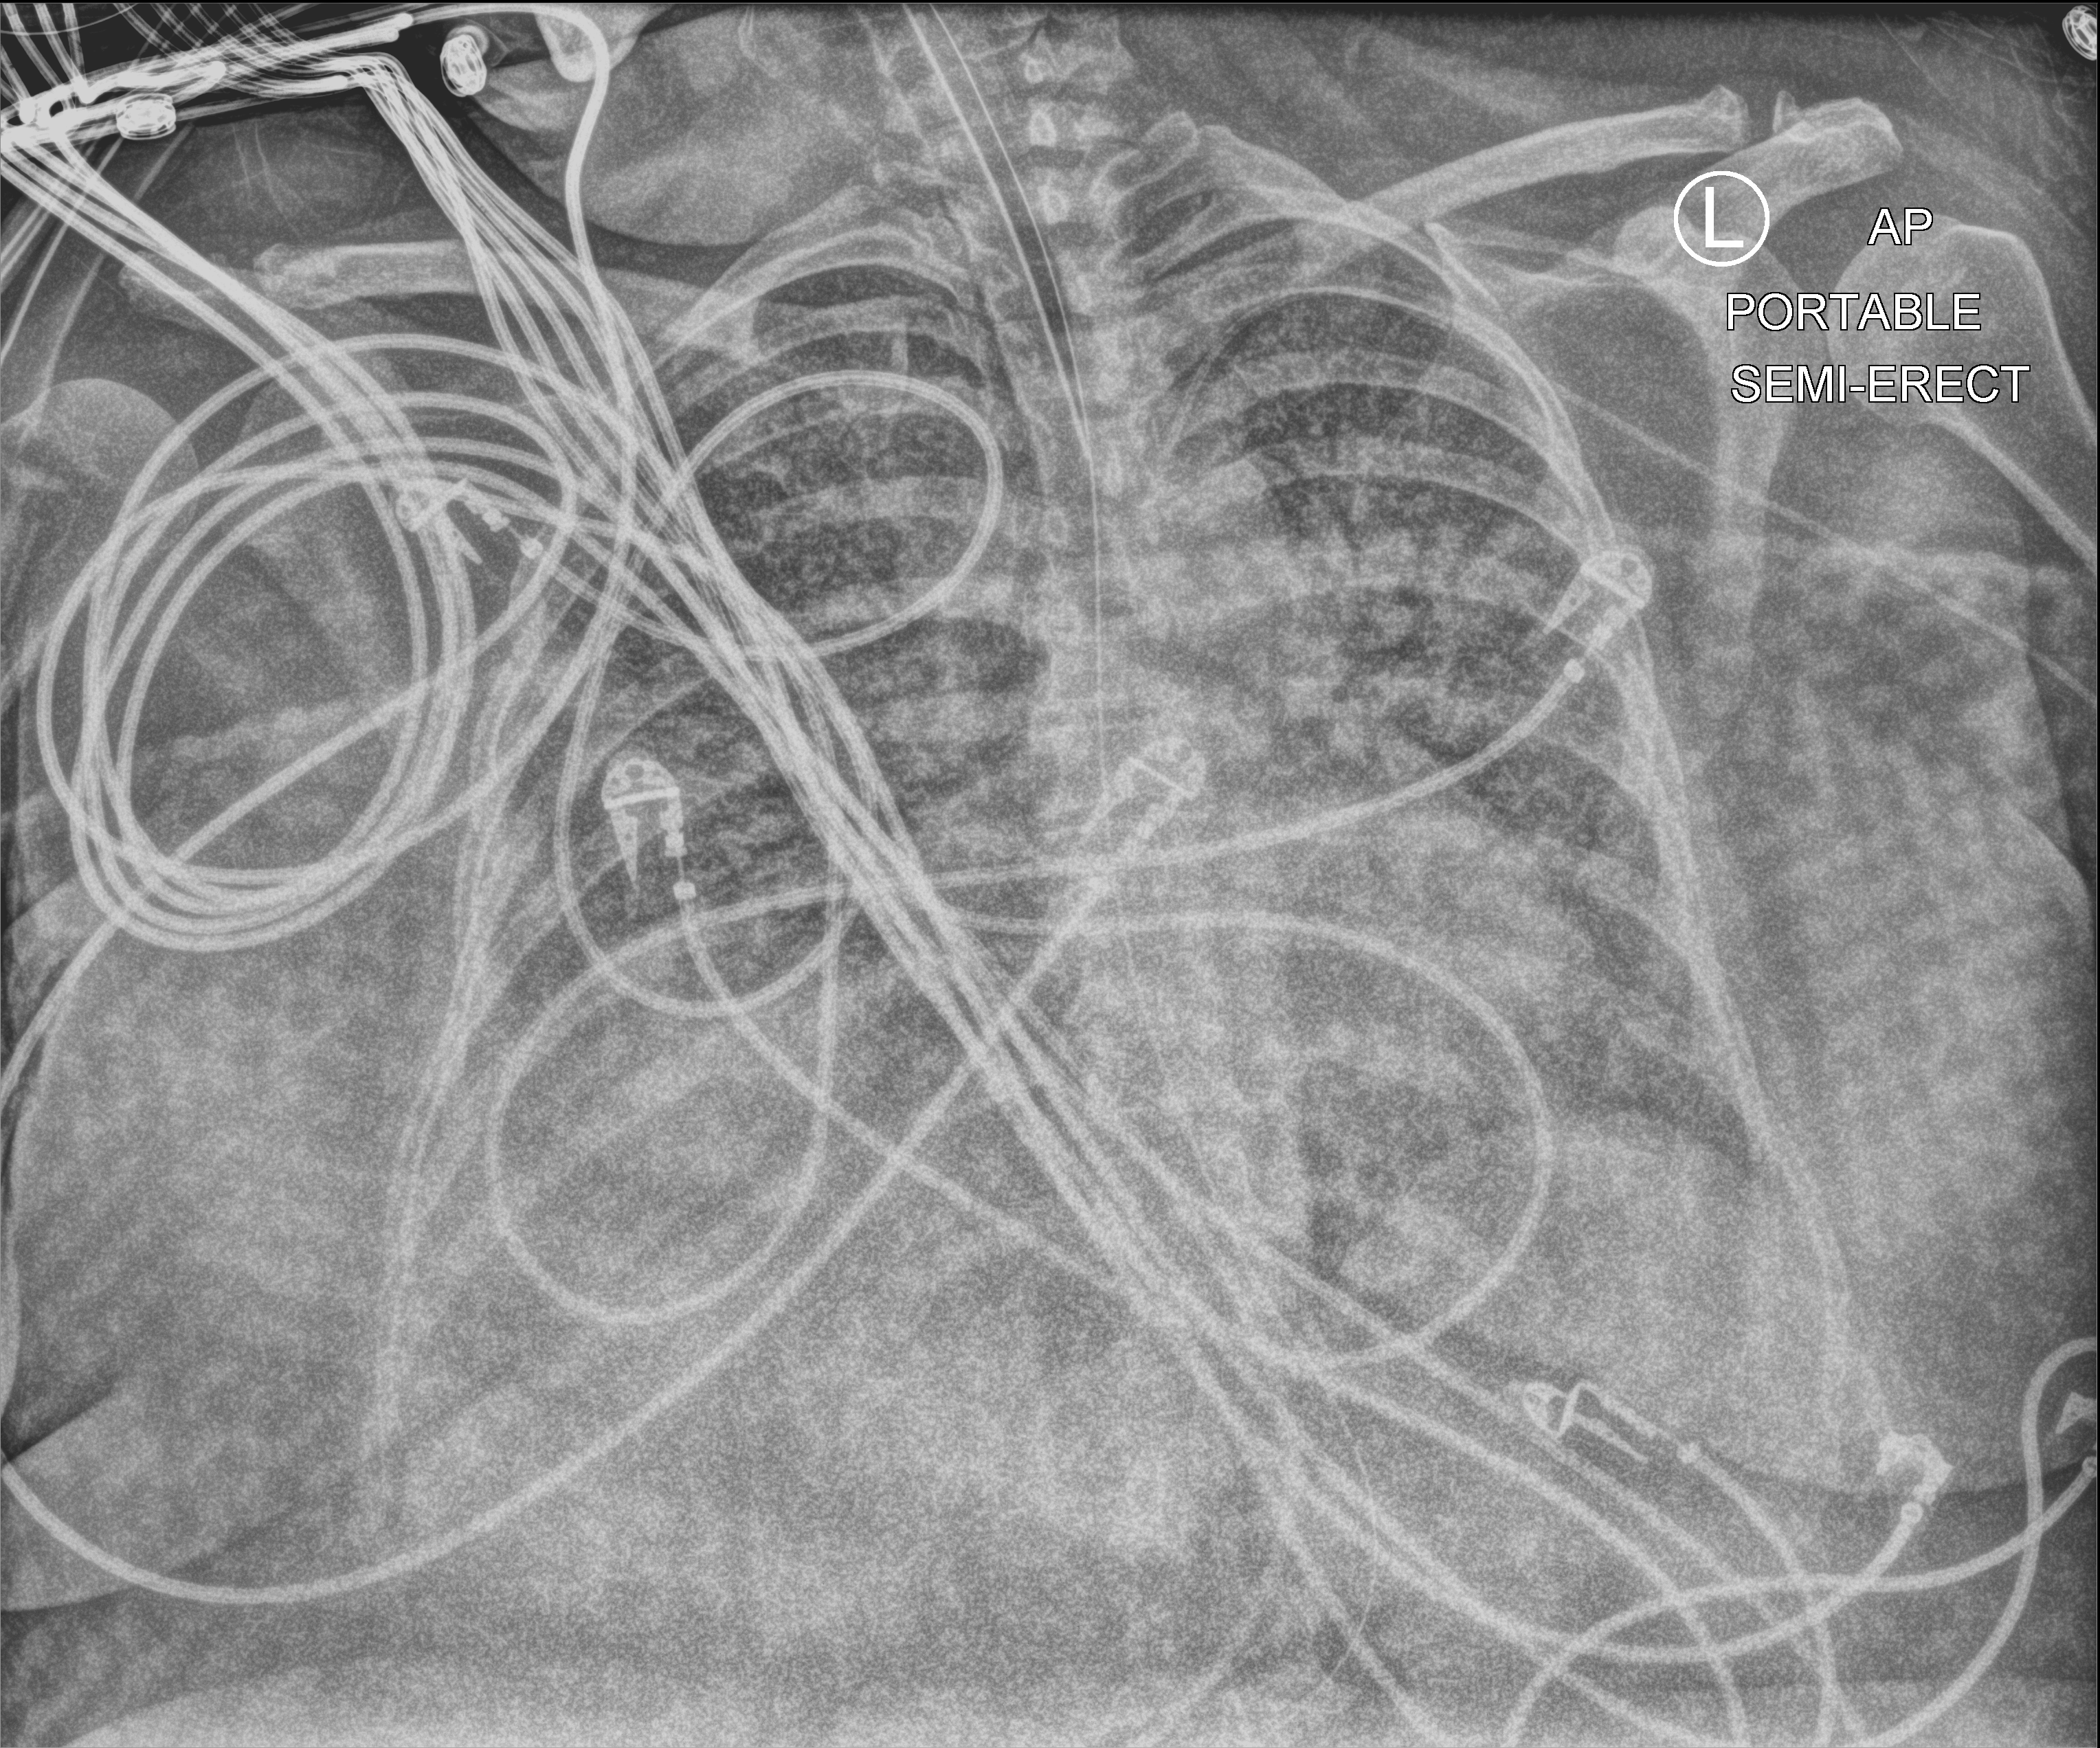
Bedside chest radiograph (computed radiography), anteroposterior (AP) projection. Patient hospitalised with COVID-19; female, aged 18–59 years.
From the hospital-stay record, not from the radiograph (when in the stay this image was taken is not recorded):
- admitted to intensive care during this hospital stay: yes
- diabetes (admission record): no
- mechanically ventilated during this hospital stay: yes